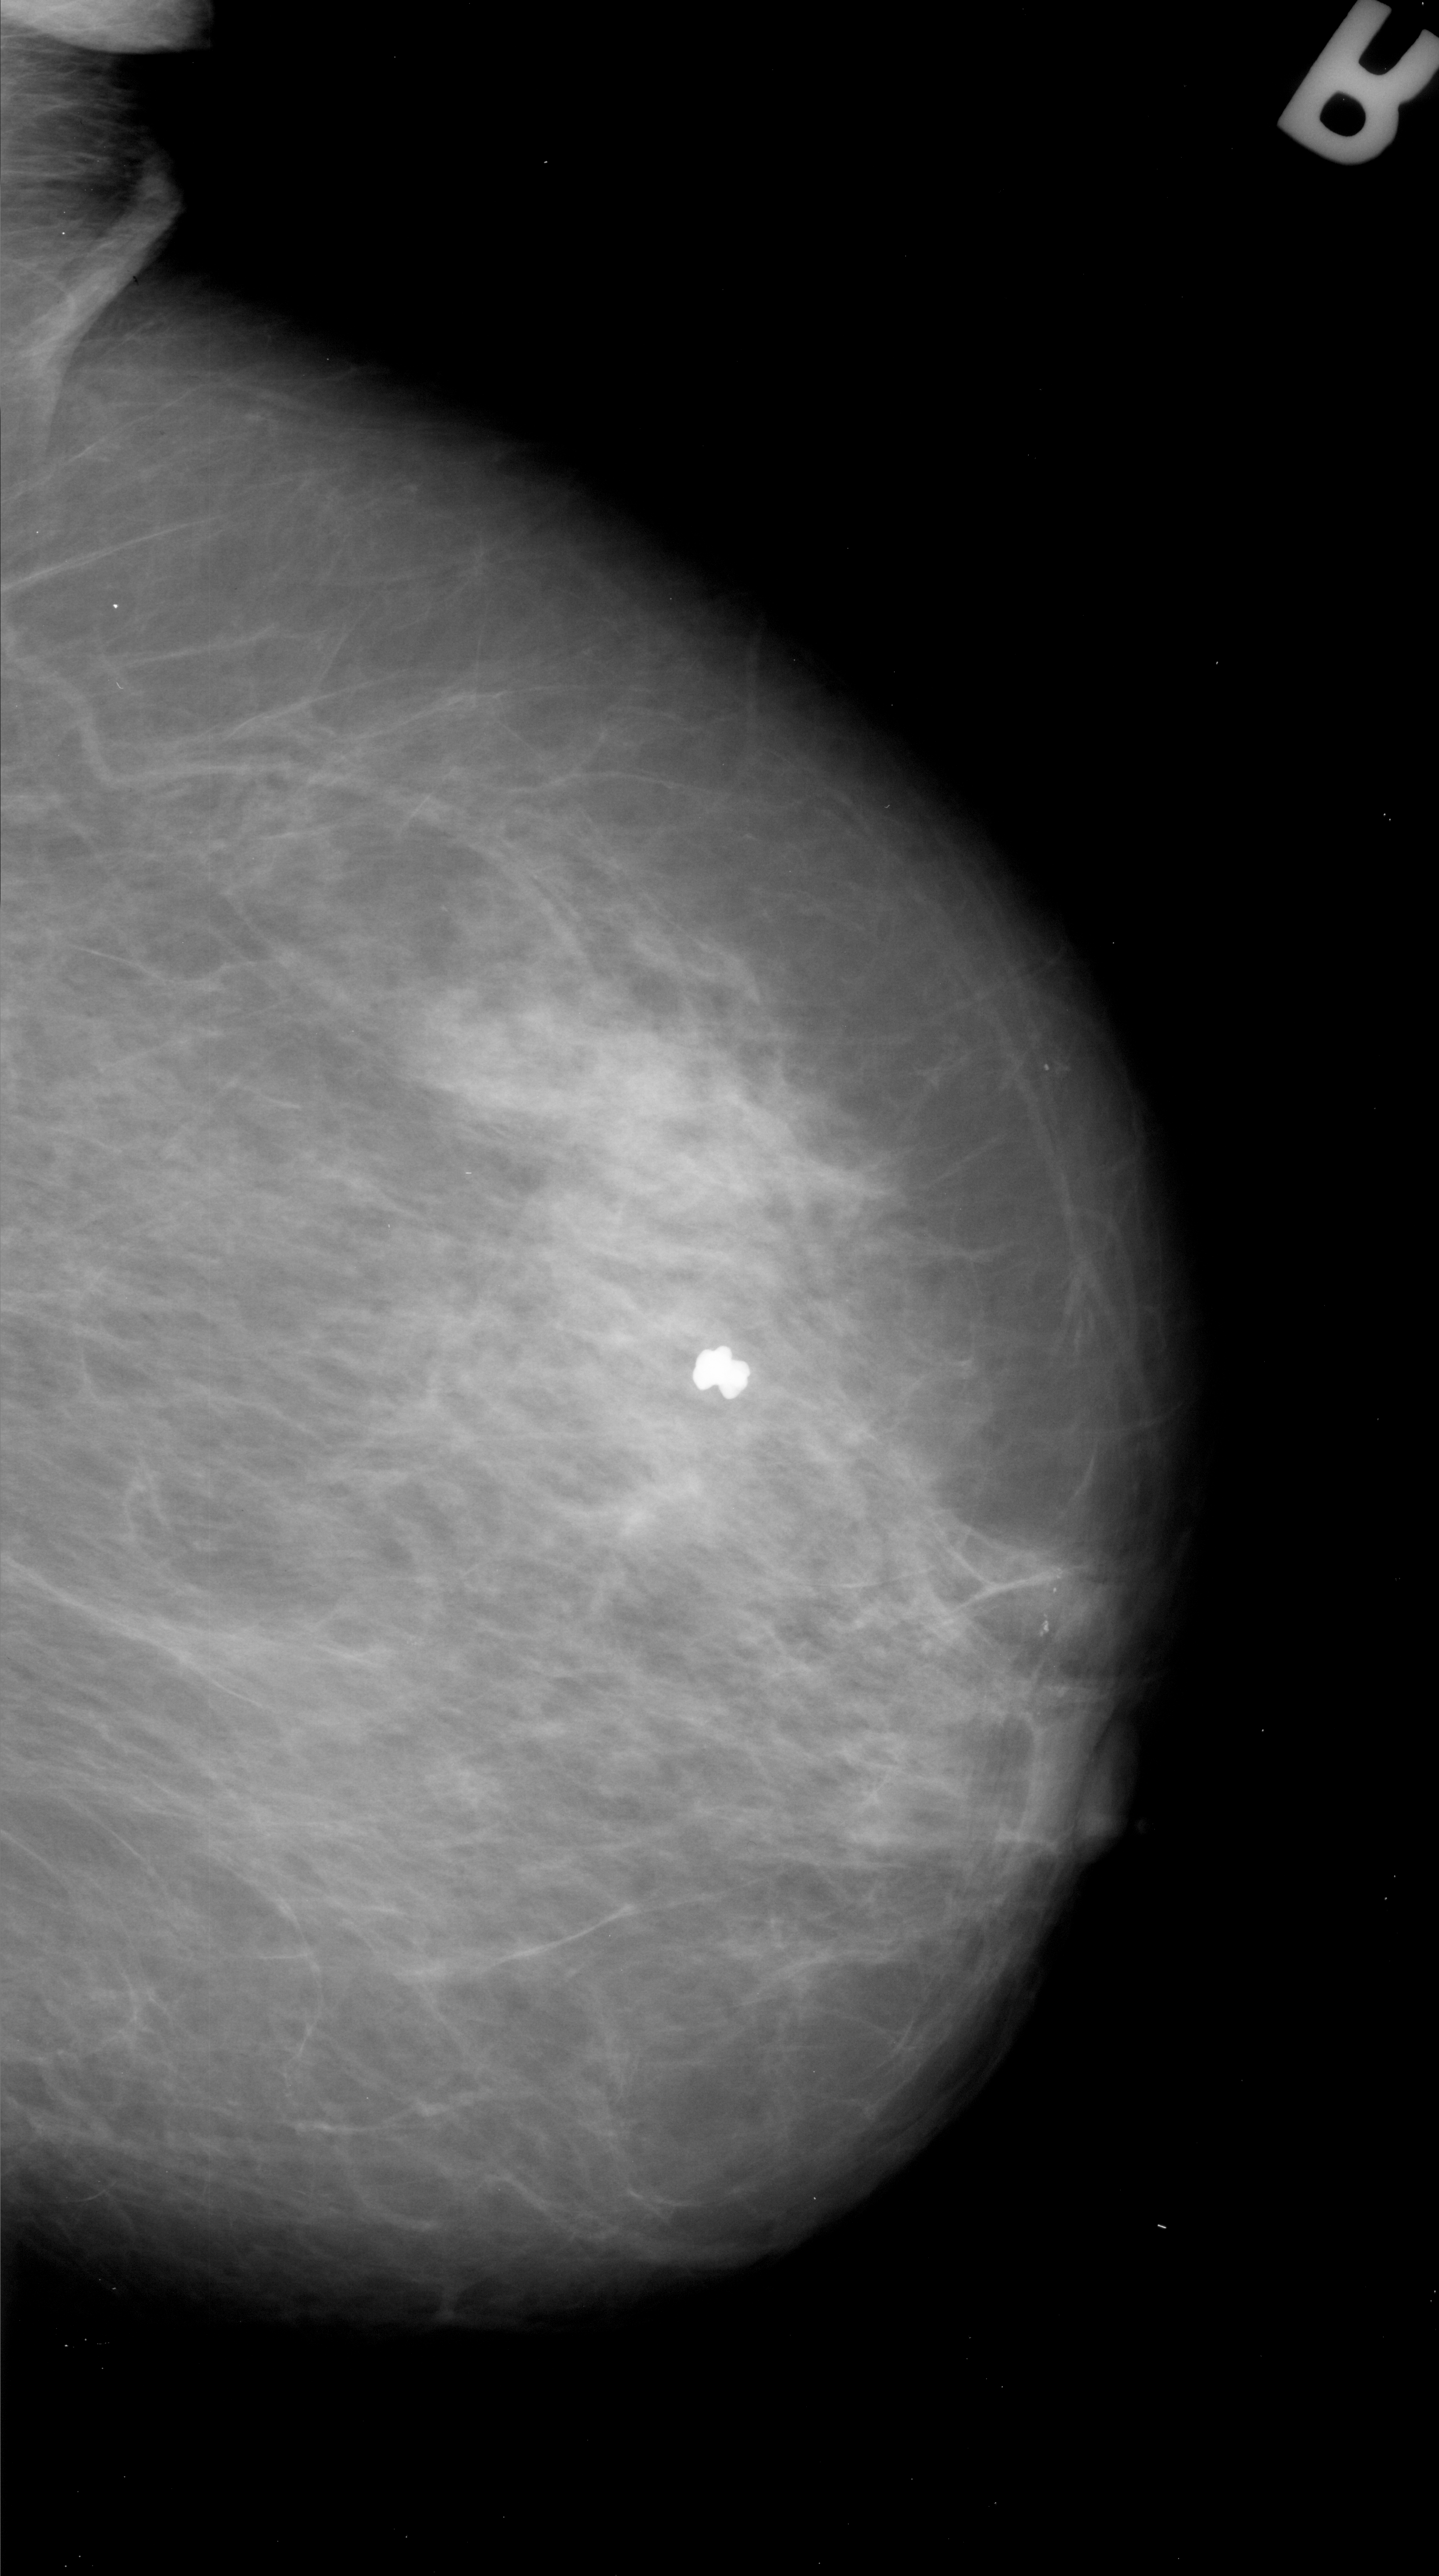
Mammogram (digitized film); right breast; MLO view; BI-RADS breast density category 3 (scale 1–4).
- Calcifications, morphology pleomorphic, distribution linear; BI-RADS assessment category 4; pathology (as recorded): malignant.